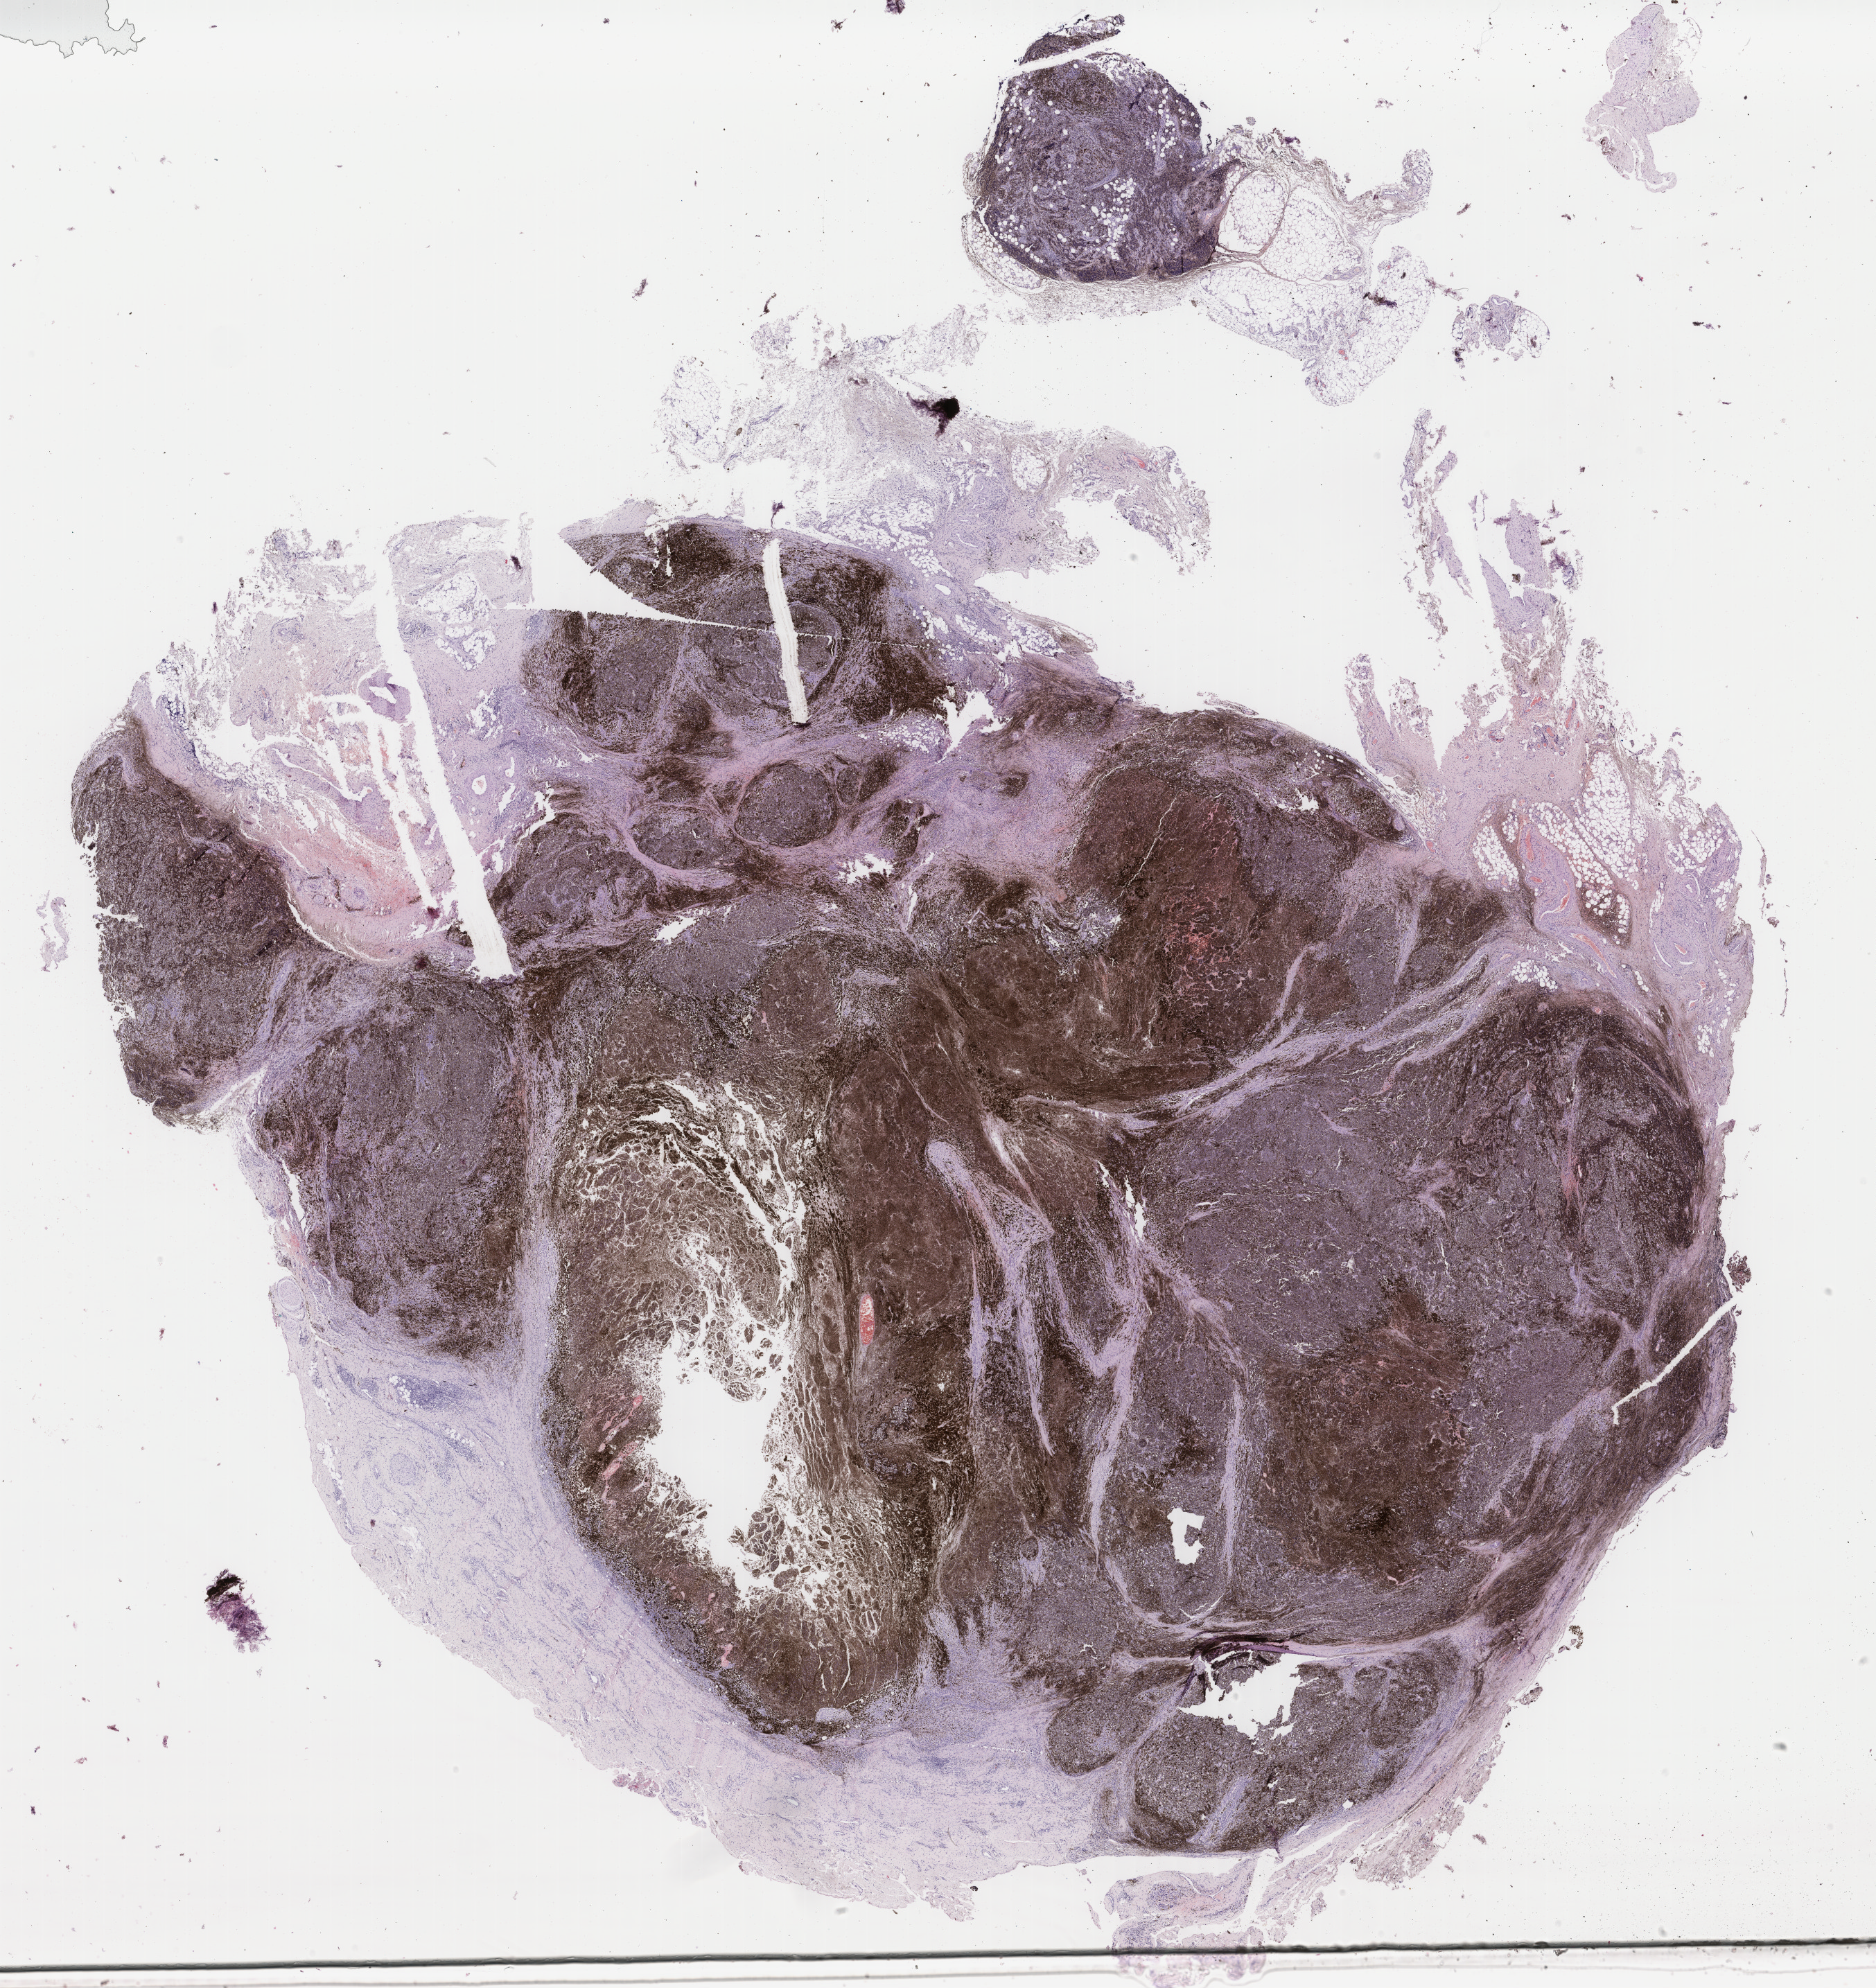
Digitized Hematoxylin and eosin (H&E) stained tissue section (whole slide) — a low-resolution overview of the entire scanned area, about 21.5 x 22.8 mm (slide scanned at 40x); formalin-fixed paraffin-embedded (FFPE) diagnostic section; metastatic tumour sample. Male patient; age at initial diagnosis 54 years.
This section: metastatic tumour tissue. Patient diagnosis: Malignant melanoma, NOS.